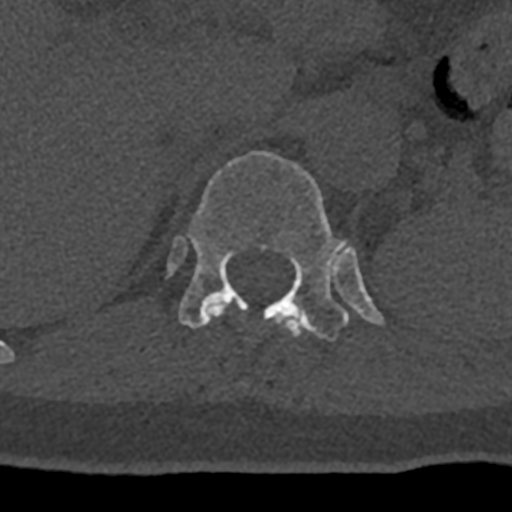
CT including the spine, one axial slice. Position 505 of 797 along the scan axis. 120 kVp. Bone window (W 1800 / L 400 HU). 0.5 mm slice thickness. 512 × 512 image matrix. Male patient, age 74 years. From the clinical record (not read from this slice): primary cancer: renal; vertebrae with lytic lesions (as recorded): T10, L1, L2, L3, L4, L5.
Structures marked on this image (semi-automatically segmented with operator editing):
- T11 vertebra: box from (x=208, y=303) to (x=304, y=337) px
- T12 vertebra: (x=168, y=151)–(x=384, y=341)